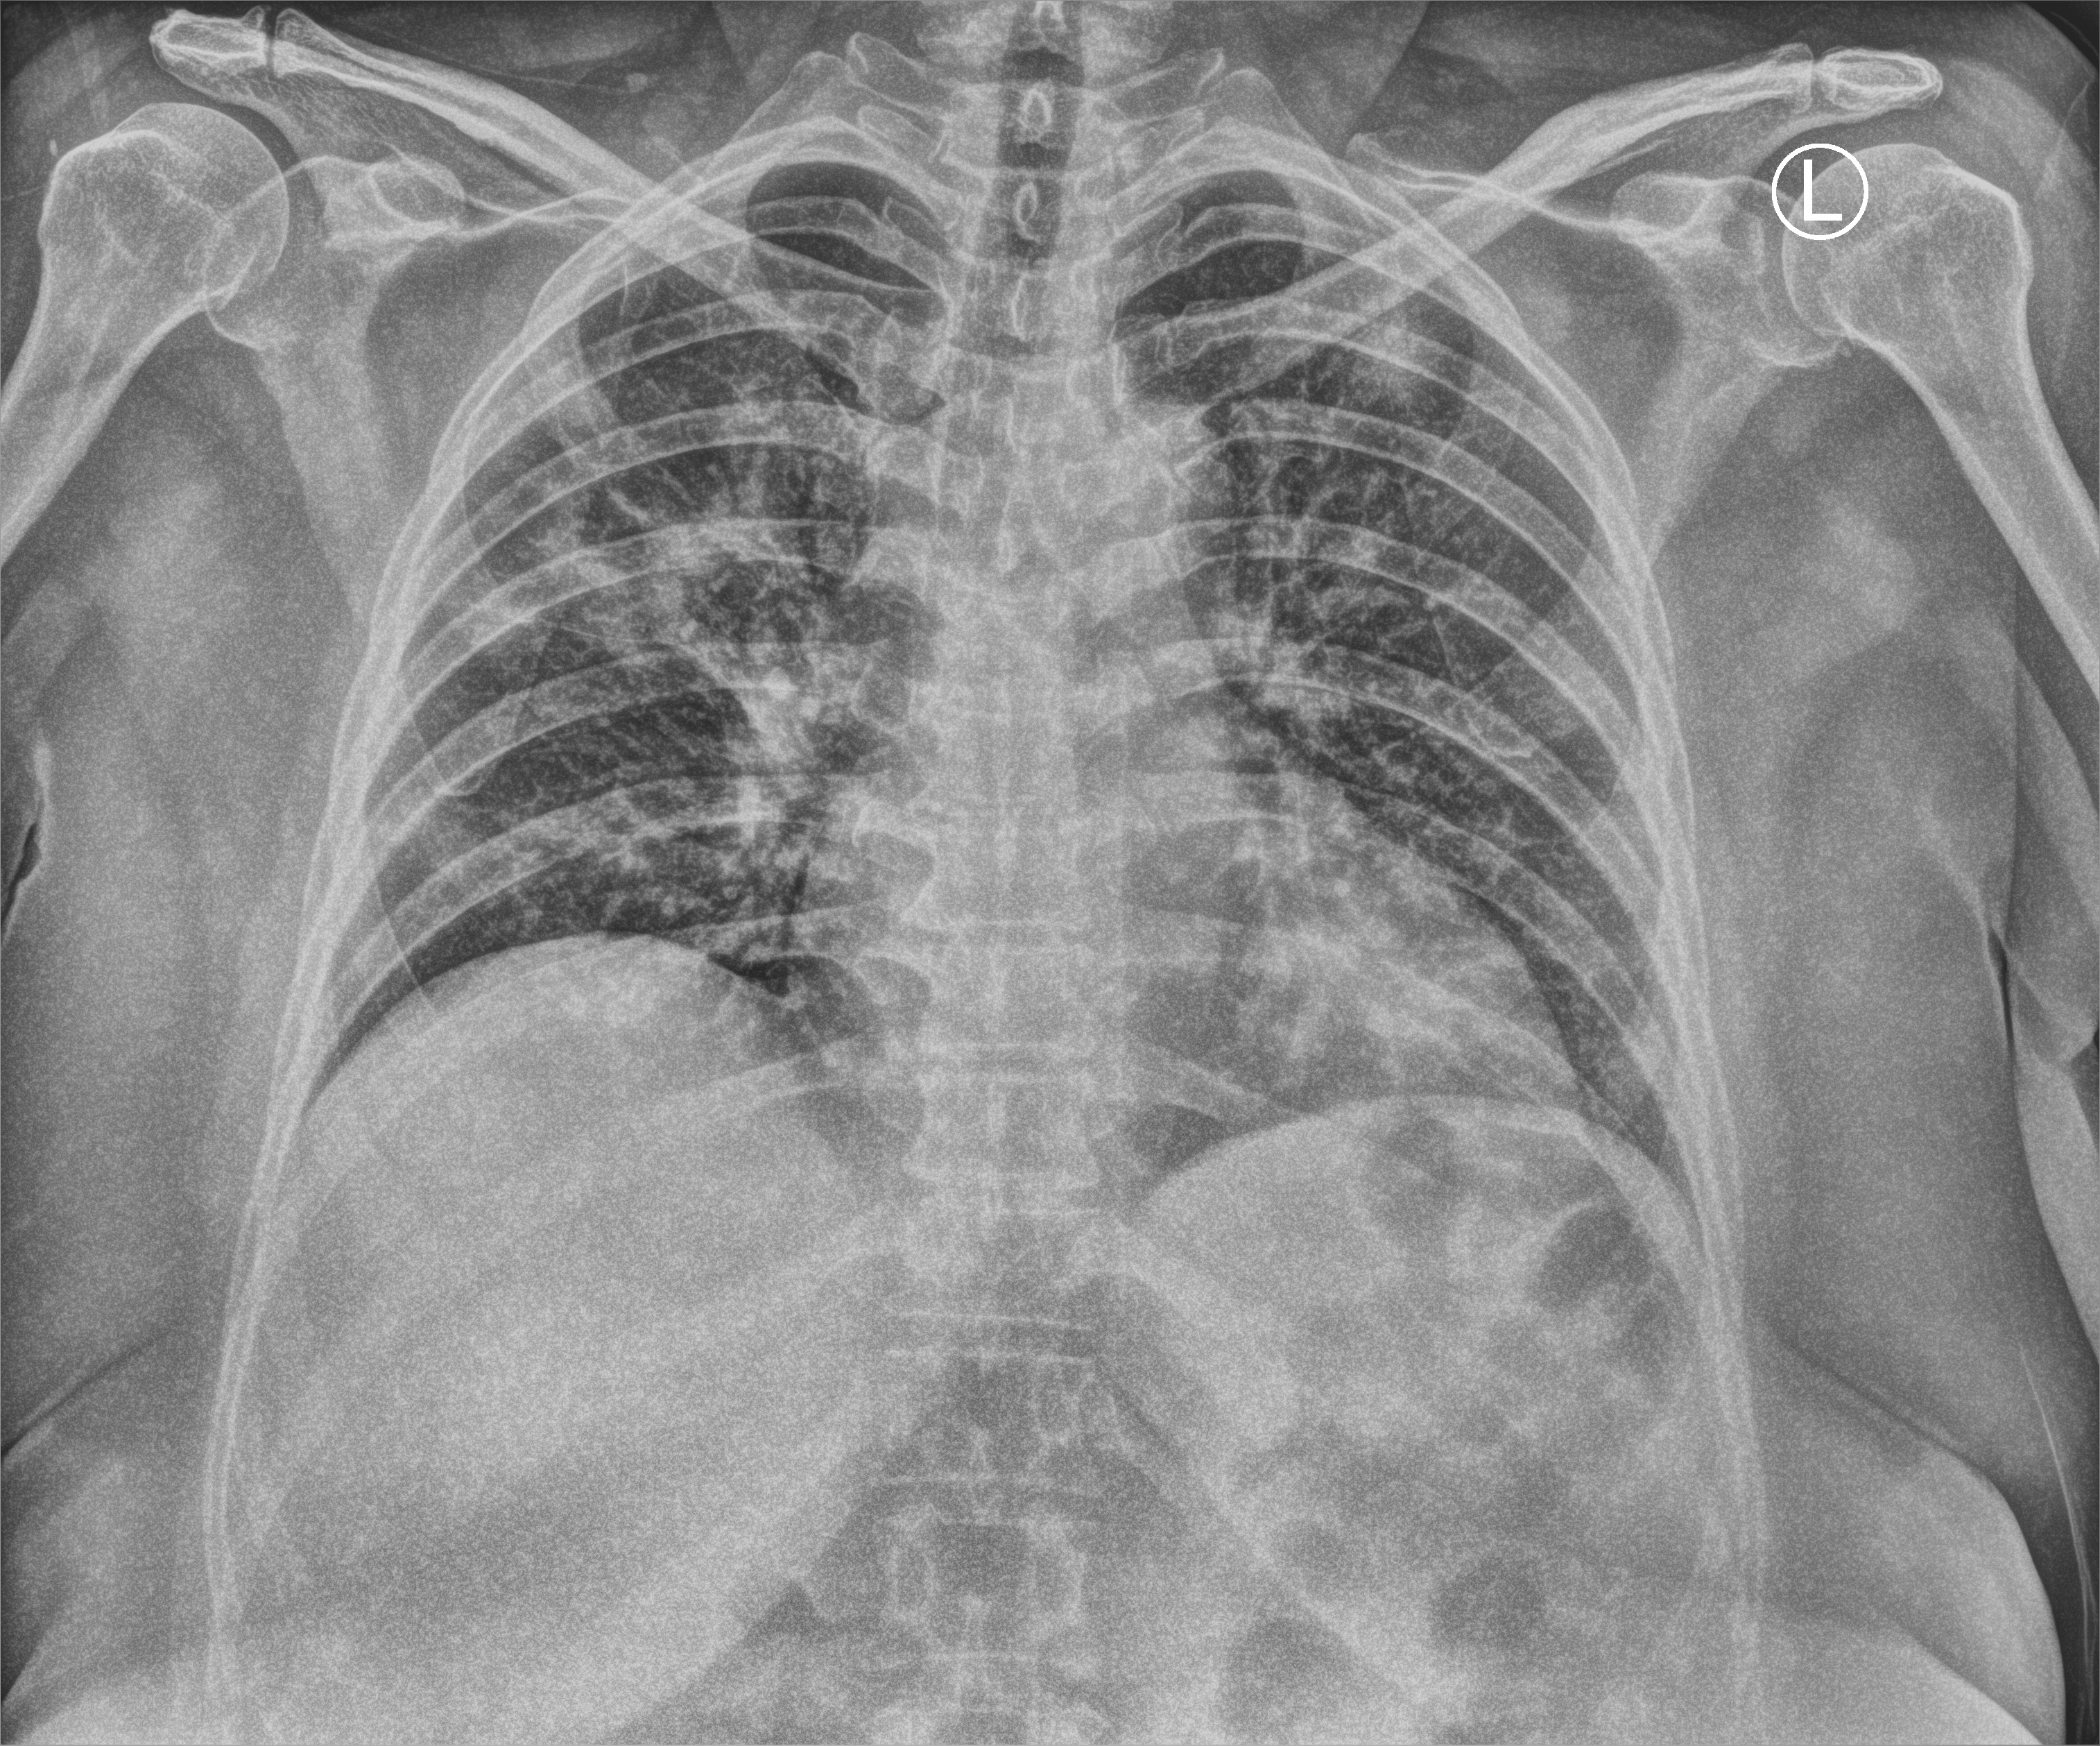
Chest X-ray (portable); anteroposterior (AP) projection. Patient hospitalised with COVID-19; female, aged 60–74 years.
From the hospital-stay record, not from the radiograph (when in the stay this image was taken is not recorded): admitted to intensive care during this hospital stay: no; mechanically ventilated during this hospital stay: no.